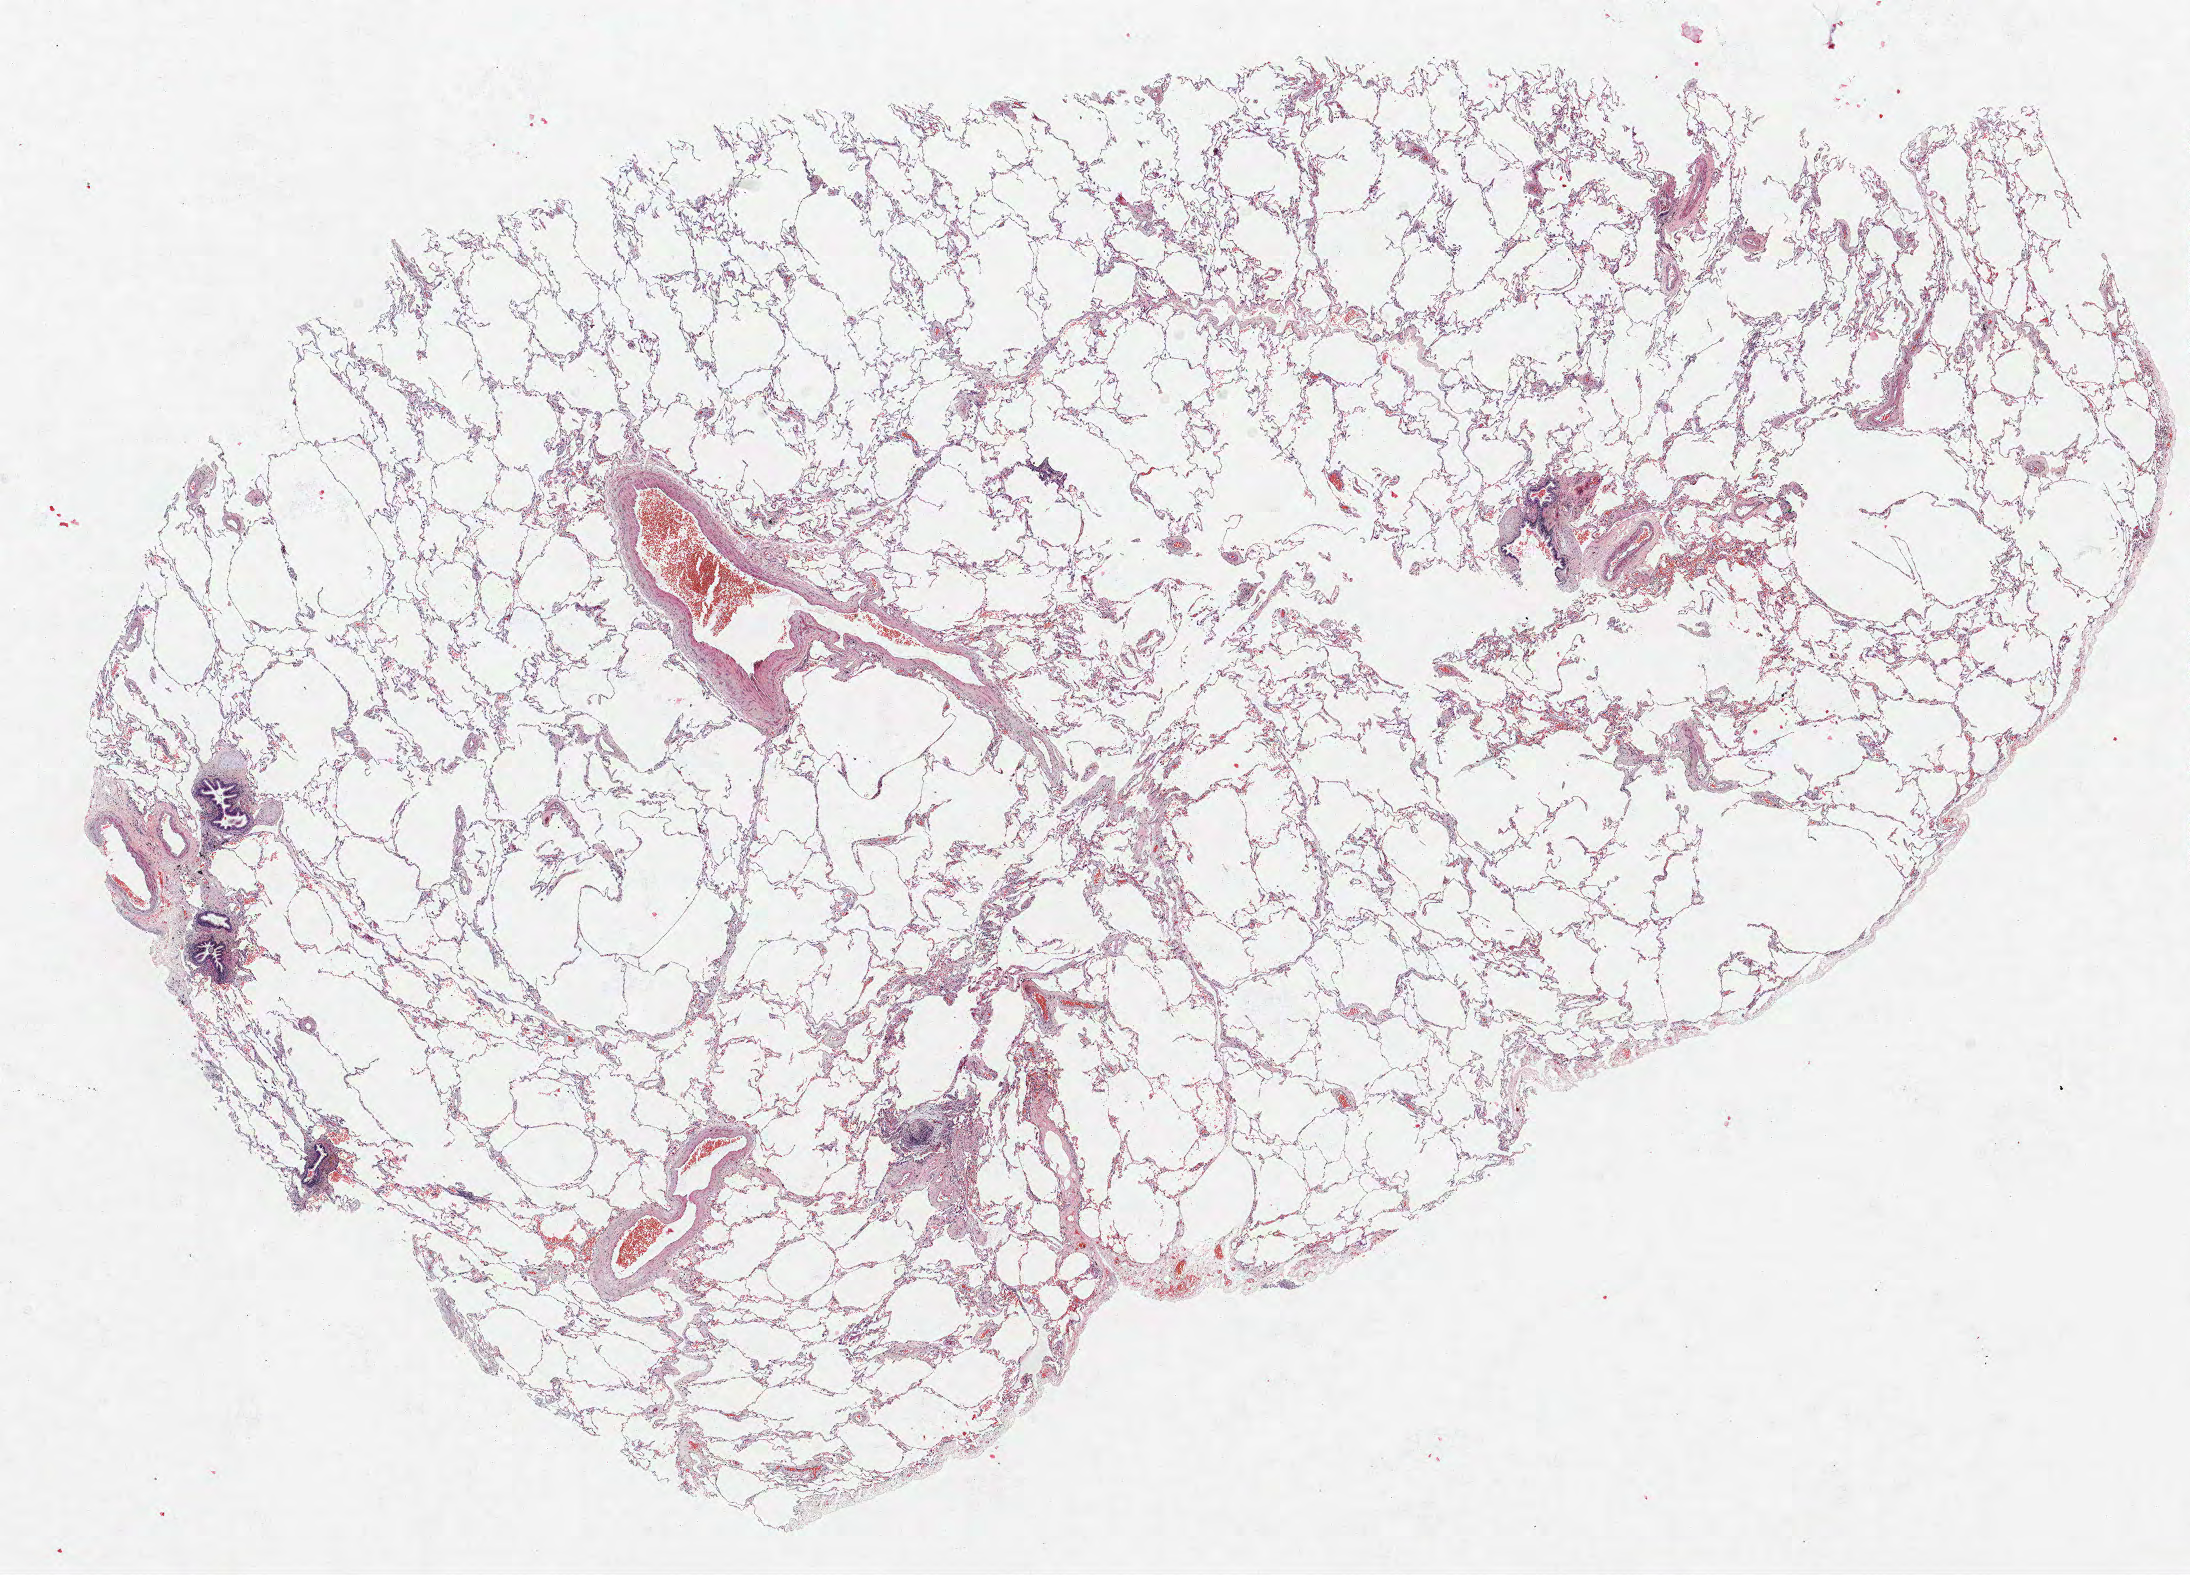
Hematoxylin and eosin (H&E) stained whole-slide image, shown as a low-resolution overview of the whole scanned area (about 17.5 x 12.6 mm, from a 40x scan), formalin-fixed paraffin-embedded (FFPE) section, lung. Male, age 71 at enrolment. Grade: moderately differentiated (G2).
Primary tumour location (clinical record): left upper lobe. Tumour size (pathology): 35 mm. Stage (AJCC 6th edition): IIB. Participant's lung-cancer diagnosis: Bronchiolo-alveolar adenocarcinoma, NOS (ICD-O-3 8250/3).